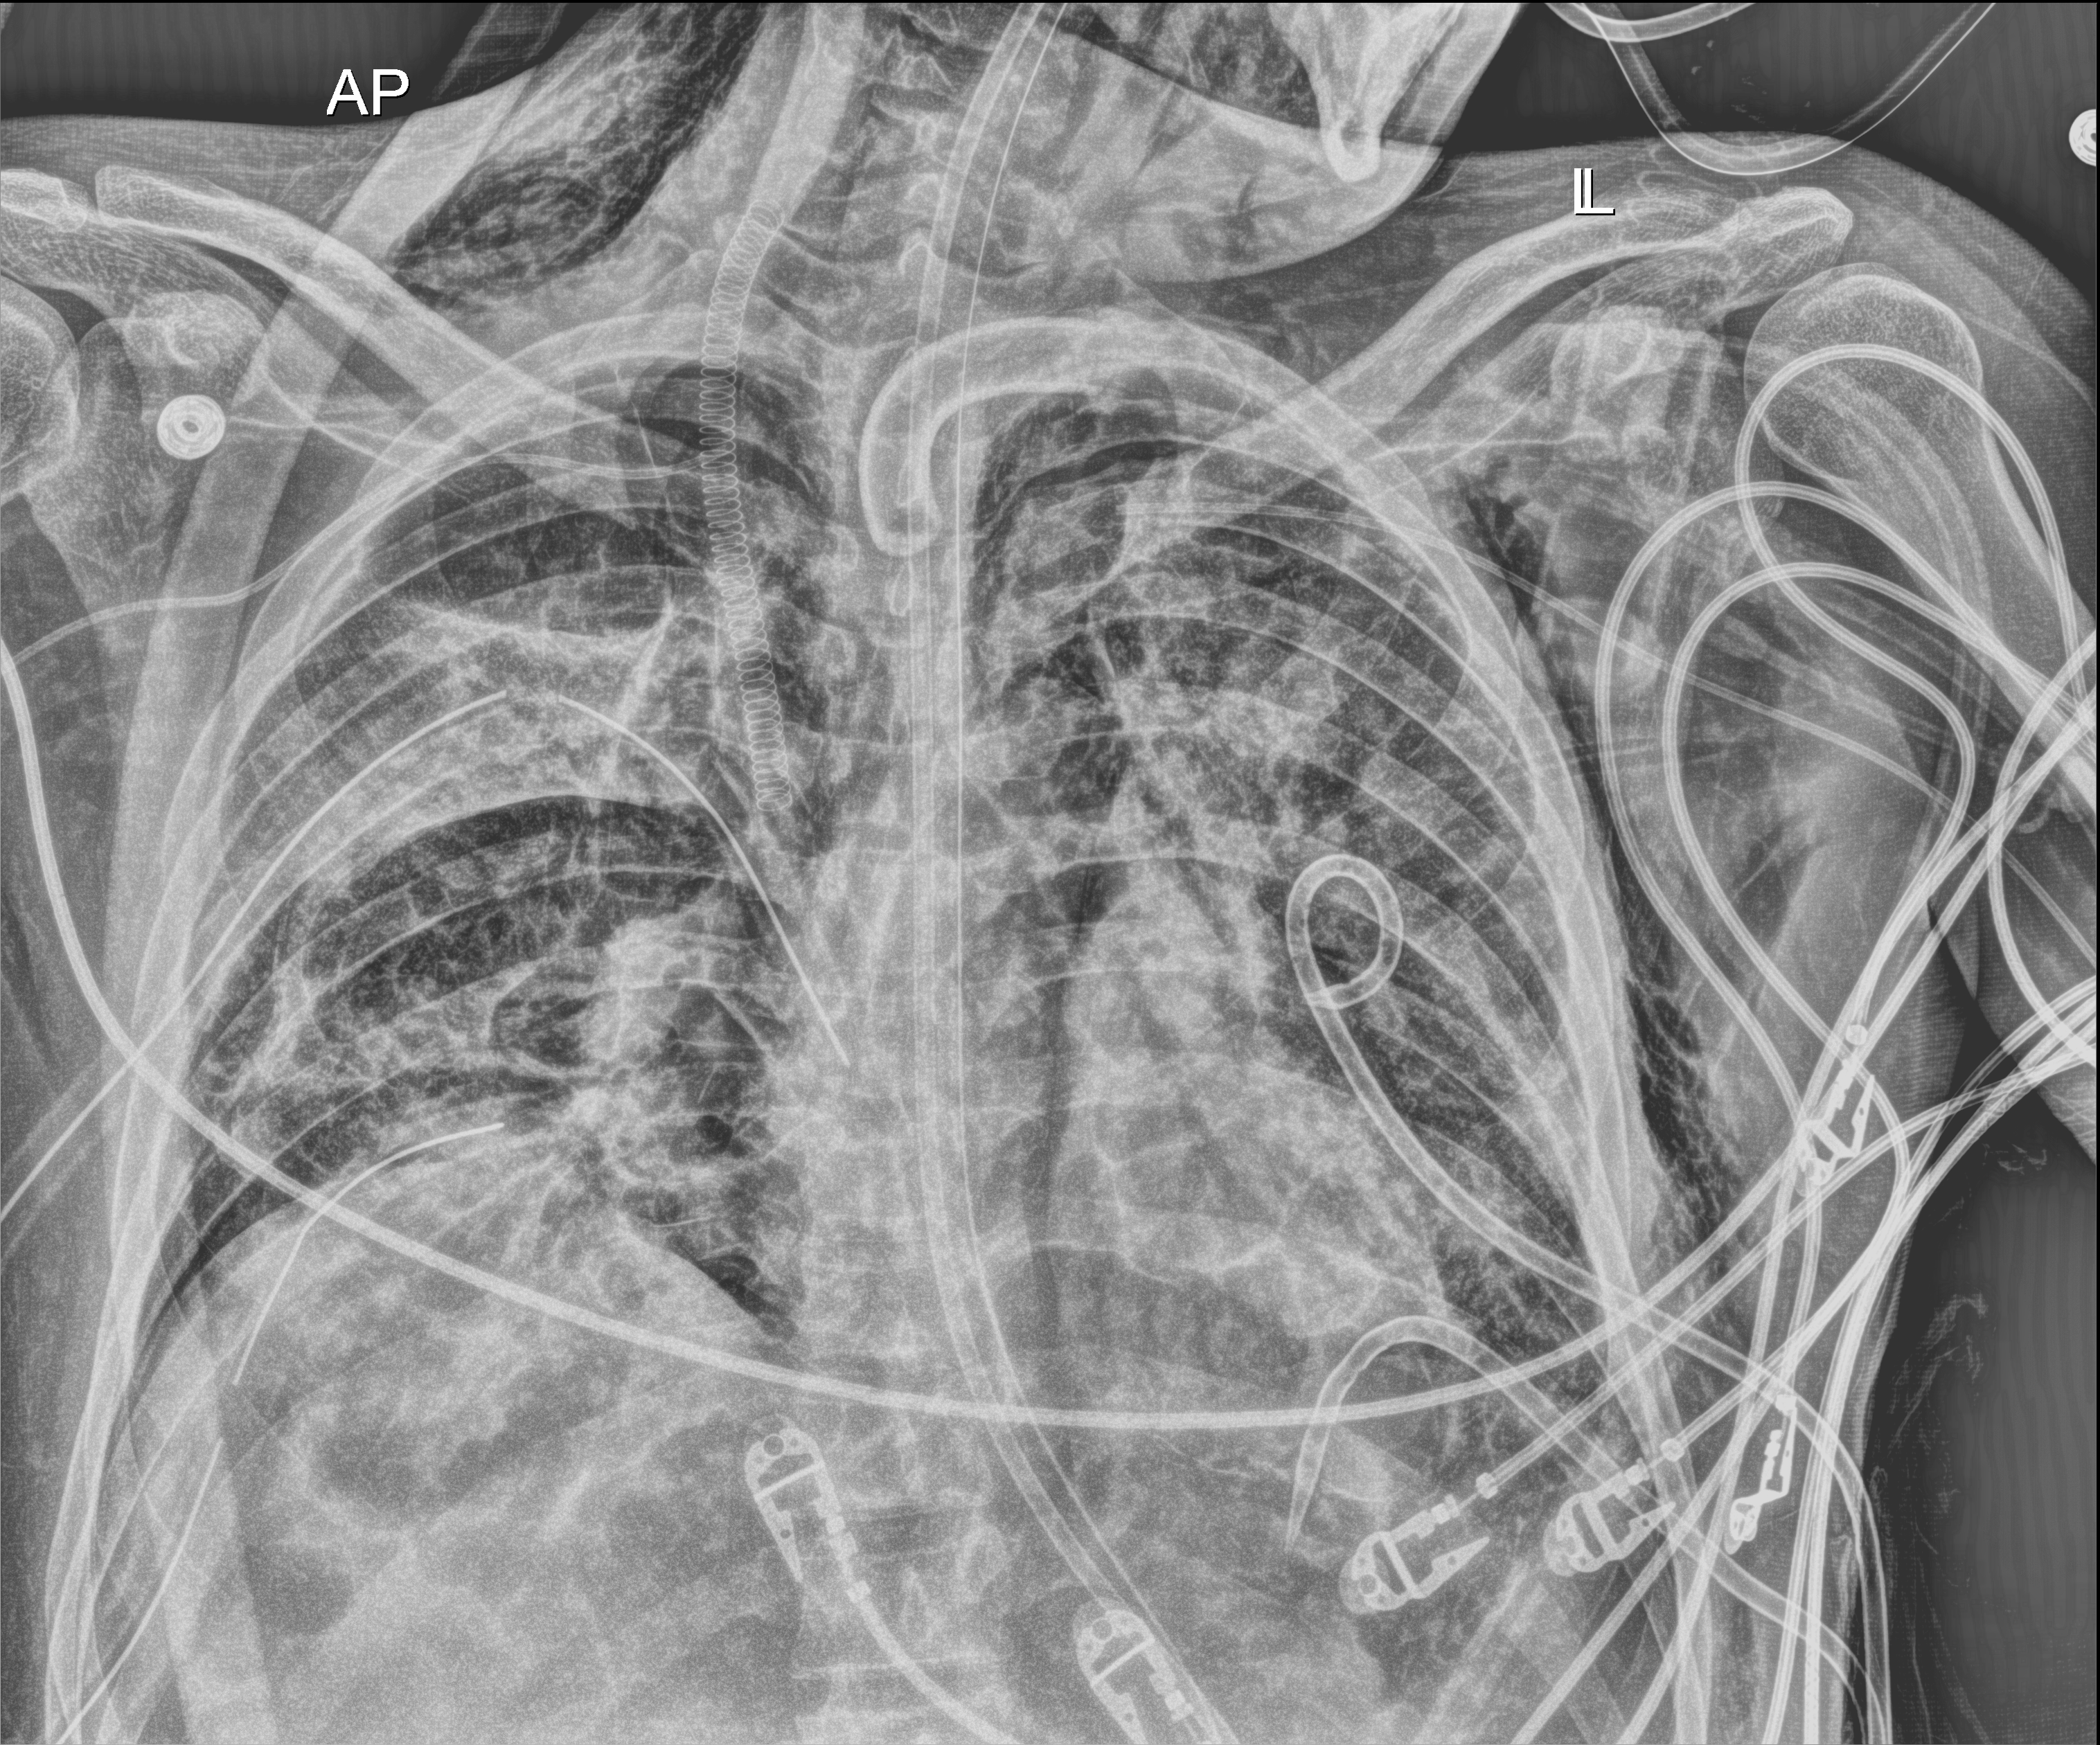
Chest radiograph (digital radiography); anteroposterior (AP) projection. Adult patient hospitalised with COVID-19, age 18–59 years.
Admission-level facts for this patient (not findings on this image; timing relative to this image not recorded): length of hospital stay: 60 days.